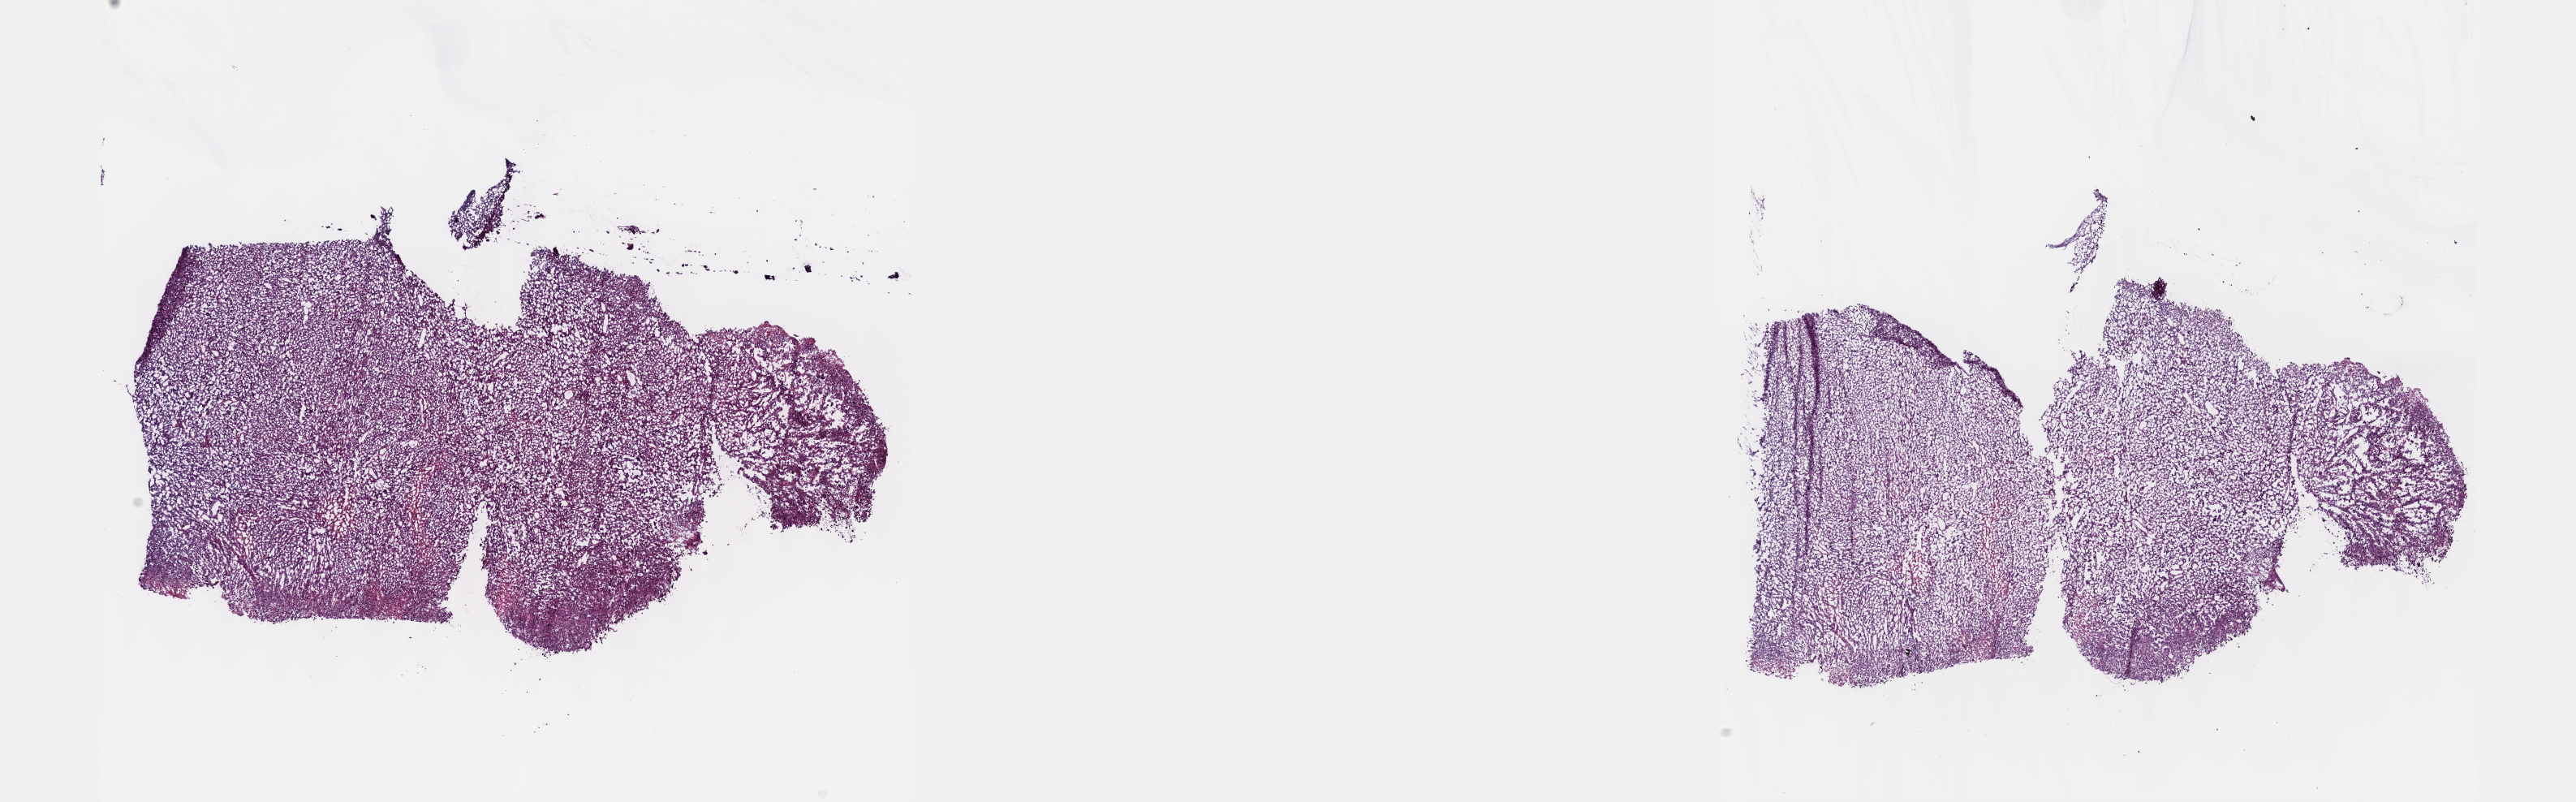
Whole-slide histology image, H&E-stained, a low-resolution overview of the entire scanned area, about 25.7 x 8.0 mm, frozen section from the top of the tissue portion, connective, subcutaneous and other soft tissues, primary tumour sample. Patient: male, age at initial diagnosis 70 years. Pathologist review of this section (percent, as recorded): tumour cells 85%, tumour nuclei 95%, normal cells 0%, stromal cells 5%, necrosis 10%. Infiltration values recorded for this section: lymphocyte infiltration 0%, monocyte infiltration 0%, neutrophil infiltration 0%.
Pathologic diagnosis: Leiomyosarcoma, NOS (connective, subcutaneous and other soft tissues of lower limb and hip).